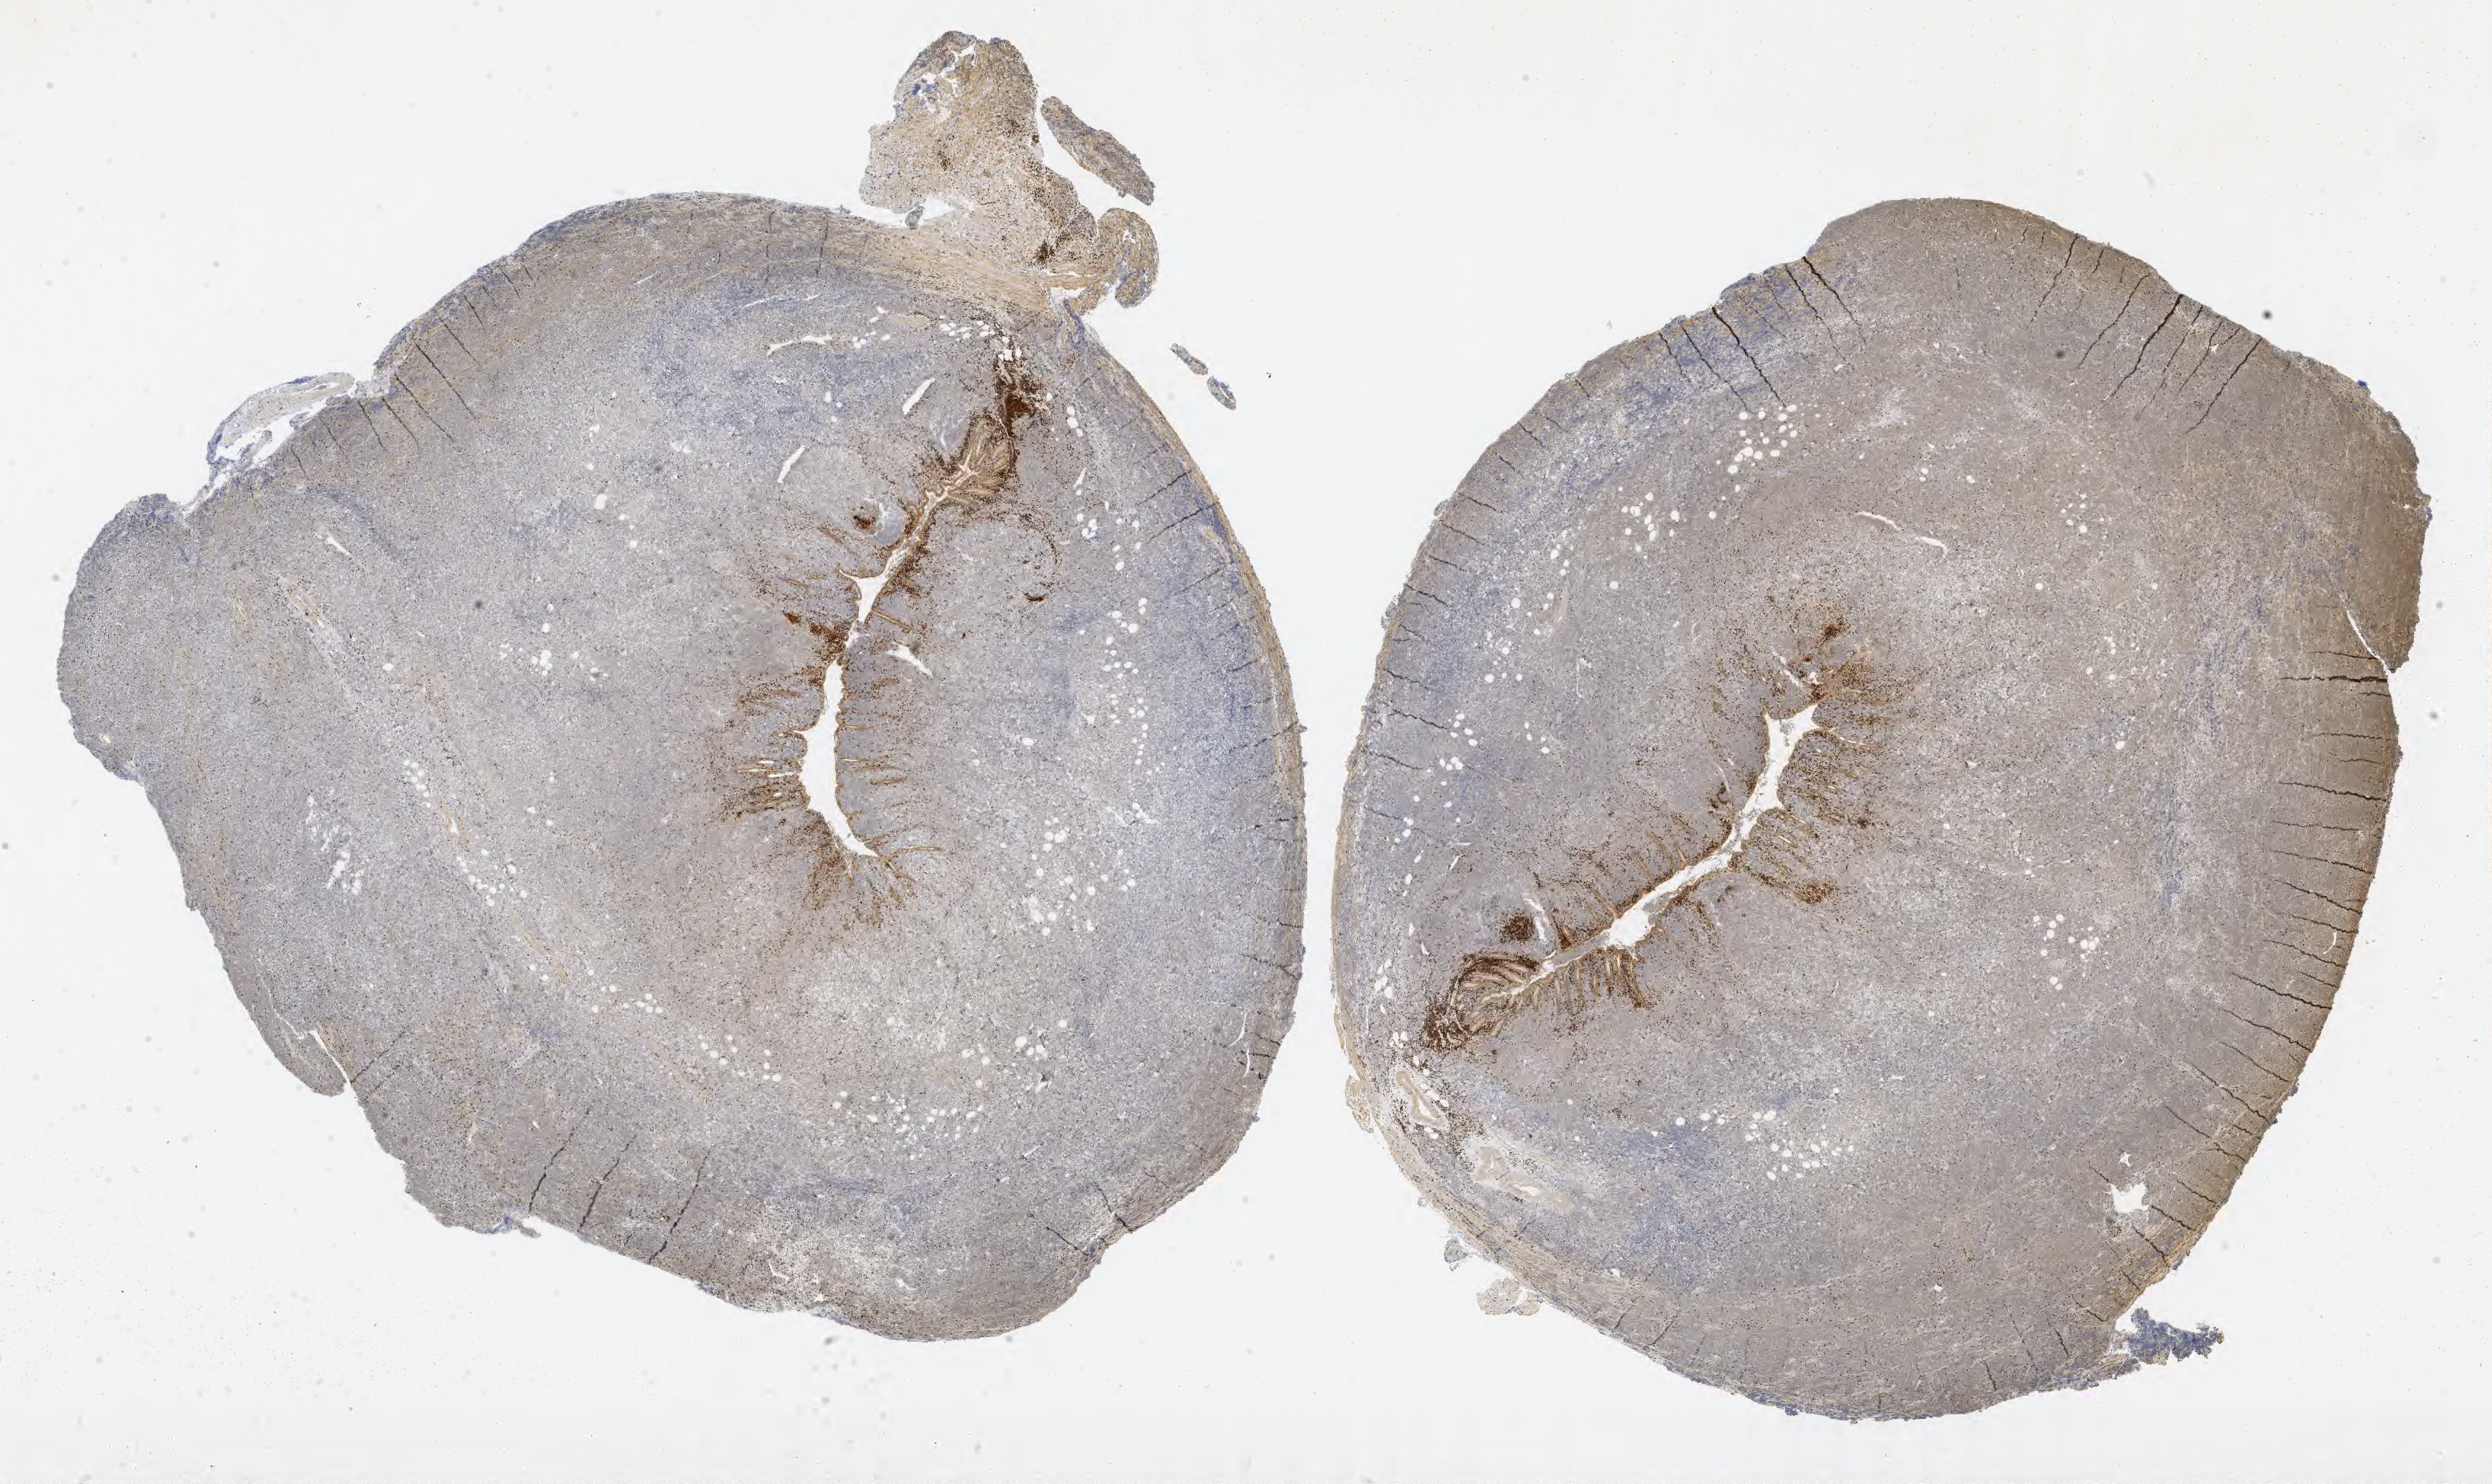
IHC for CD3, whole-slide image, shown as a low-resolution overview of the whole scanned area (about 27.7 x 16.5 mm), specimen: tumor tissue. Male patient, 63 years old.
Diagnosis: Diffuse large B-cell lymphoma, NOS.